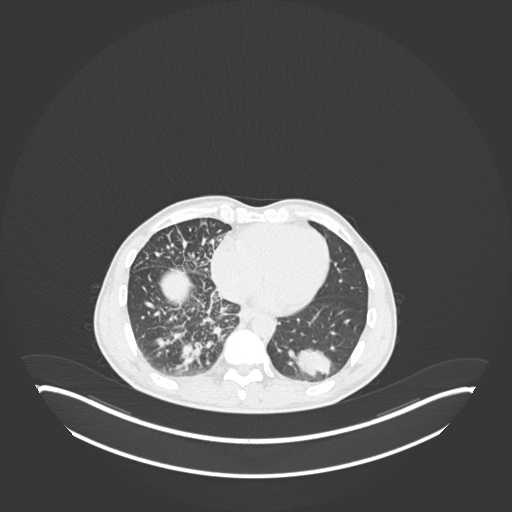
Chest CT, one axial slice. Position 72 of 237 along the scan axis. Lung window (W 1500 / L -600 HU). 512 × 512 image matrix. Patient: male, 49 years. Case-level facts recorded for this patient, not image findings: clinical TNM (as recorded): T2b N1 M0.
Outlined on this slice (bounding box drawn by a radiologist):
- lung tumour (recorded histology: adenocarcinoma): bounding box [x1, y1, x2, y2] px = [287, 344, 337, 385]